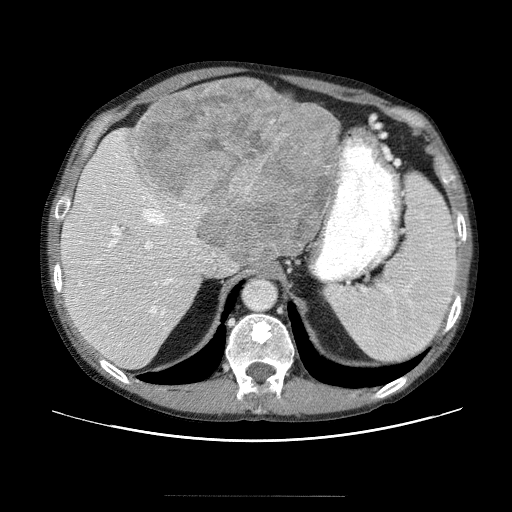
Contrast-enhanced abdominal CT (liver protocol), one axial slice; slice 37 of 69 in the series (ordered by position); 120 kVp; soft-tissue window (W 400 / L 40 HU); 512 × 512 image matrix. Case-level facts recorded for this patient, not image findings: diagnosis: hepatocellular carcinoma (patient treated with transarterial chemoembolisation; whether this scan precedes or follows treatment is not stated here); TNM stage (as recorded): Stage-IVB; Child-Pugh class: B; tumour differentiation: poorly differentiated; tumour nodularity: multinodular.
Outlined on this slice (semi-automatically segmented with operator editing):
- abdominal aorta: bounding box <244,279,275,309> (left, top, right, bottom; pixels)
- liver parenchyma outside the tumour (the mass and vessels are separate outlines, so this box may not span the whole liver): <60,86,334,370>
- mass: <135,77,340,258>
- liver vessels: <77,158,203,356>